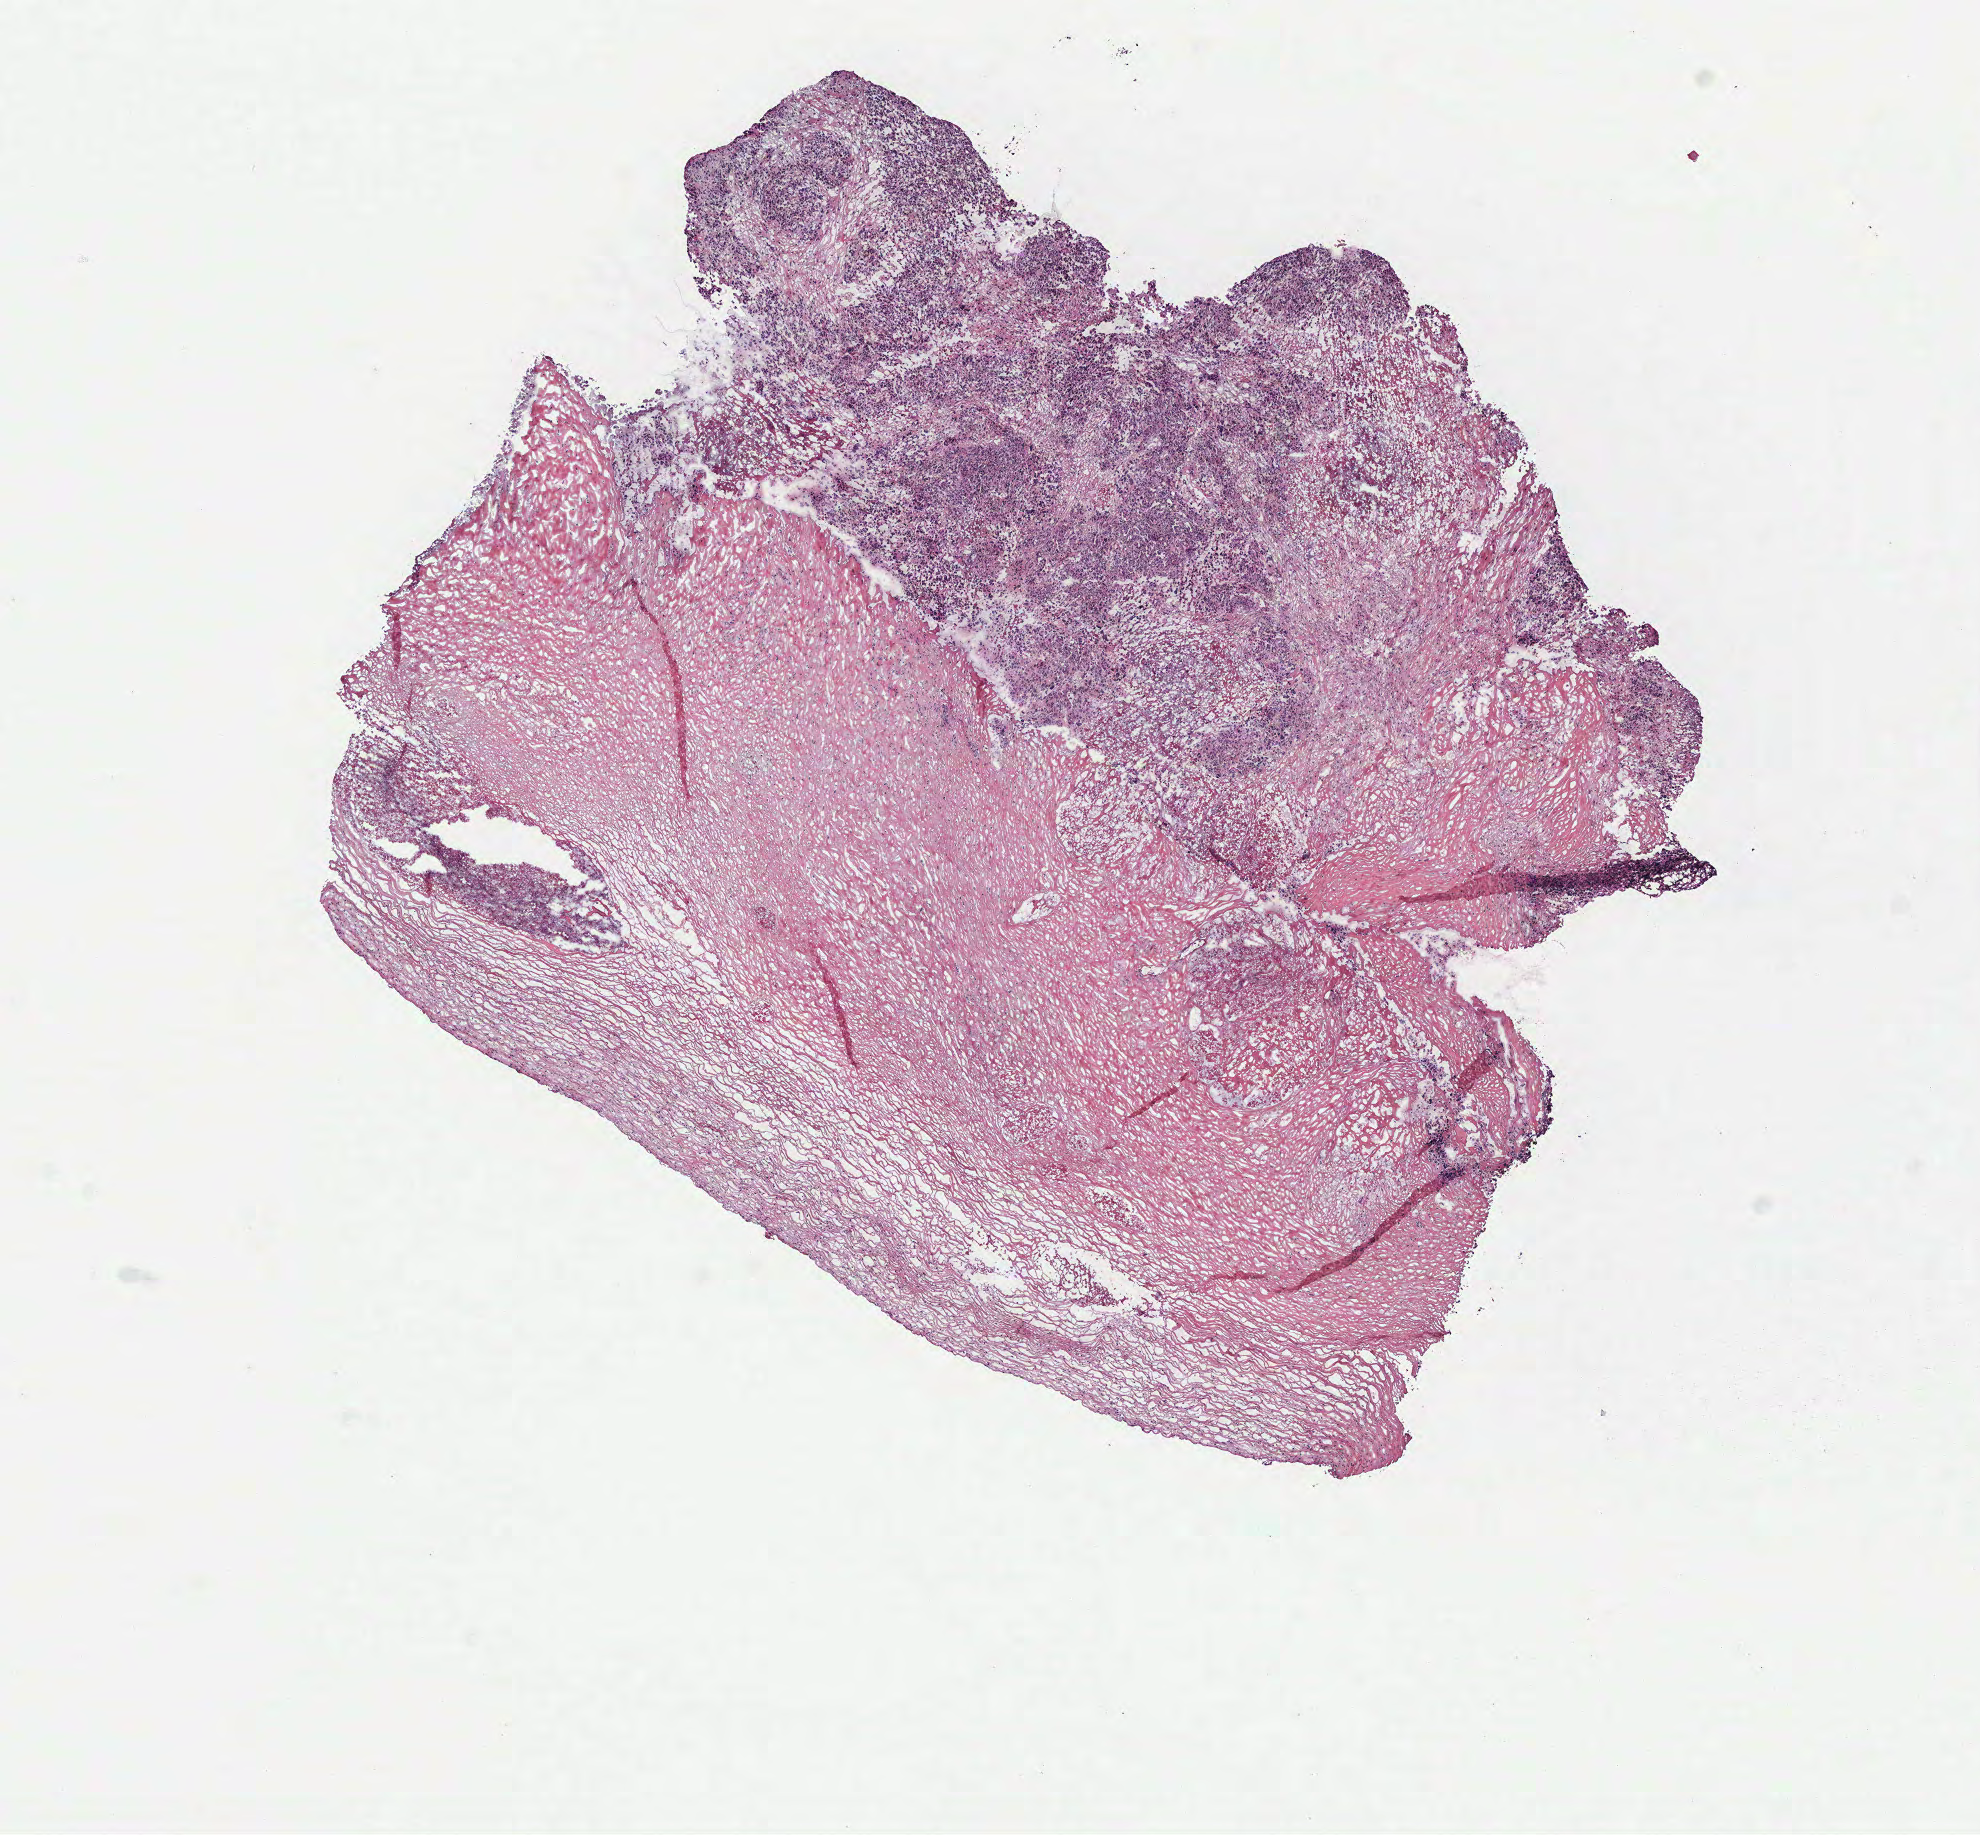
Hematoxylin and eosin (H&E) stained whole-slide image — low-resolution overview of the scanned area, about 7.9 x 7.3 mm. Ovary, tissue type not recorded.
Patient diagnosis (cohort enrolment): ovarian cancer (ovary).